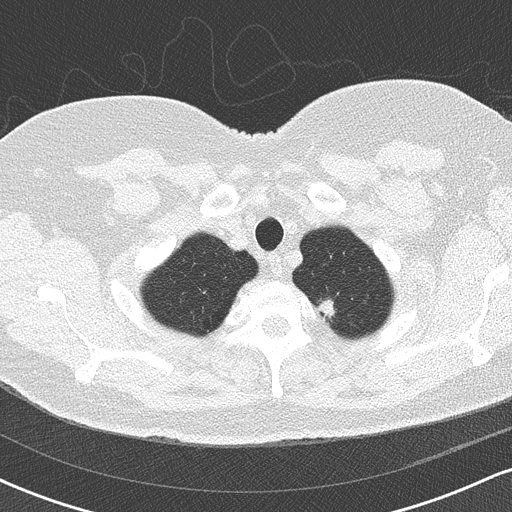
Low-dose screening chest CT, axial slice. Third screening round (two years after baseline). Lung window (W 1500 / L -600 HU). Lung (sharp) reconstruction kernel (B50f). Slice 20 of 170 in the series. 512 × 512 image matrix. Female, age 60 years at enrolment. Former smoker at enrolment.
• Expert reader's lesion annotation, bounding box [x1, y1, x2, y2] px = [299, 286, 350, 331].
• Reader record for this screening exam (exam-level; its link to the box is not recorded): non-calcified nodule or mass ≥4 mm, left upper lobe, 10 × 10 mm, soft tissue attenuation, pre-existing on the prior screen: yes.
• Later outcome: lung cancer diagnosed 94 days after this screen — non-small cell carcinoma, left upper lobe, poorly differentiated (G3), stage IB (AJCC 6th edition), 16 mm at pathology.